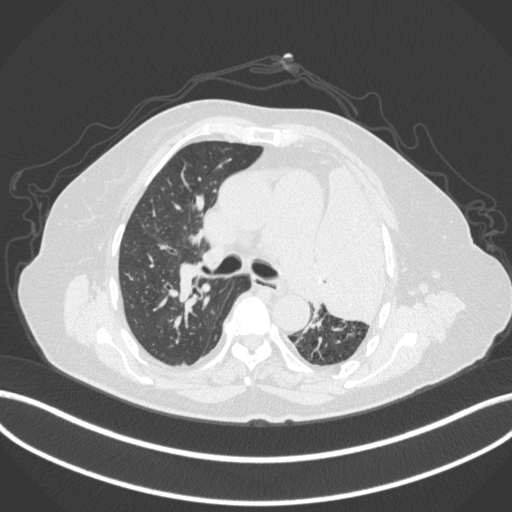
Chest CT, one axial slice; position 246 of 399 along the scan axis; reconstruction kernel B31f; 120 kVp; lung window (W 1500 / L -600 HU); 512 × 512 image matrix, field of view 400 × 400 mm. Patient: female, 75 years. Case-level facts recorded for this patient, not image findings: clinical TNM (as recorded): T3 N3 M1.
Annotated regions visible in this slice (rectangle marked by the reading radiologist):
- lung tumour (recorded histology: adenocarcinoma): bounding box <316,162,390,329> (left, top, right, bottom; pixels)